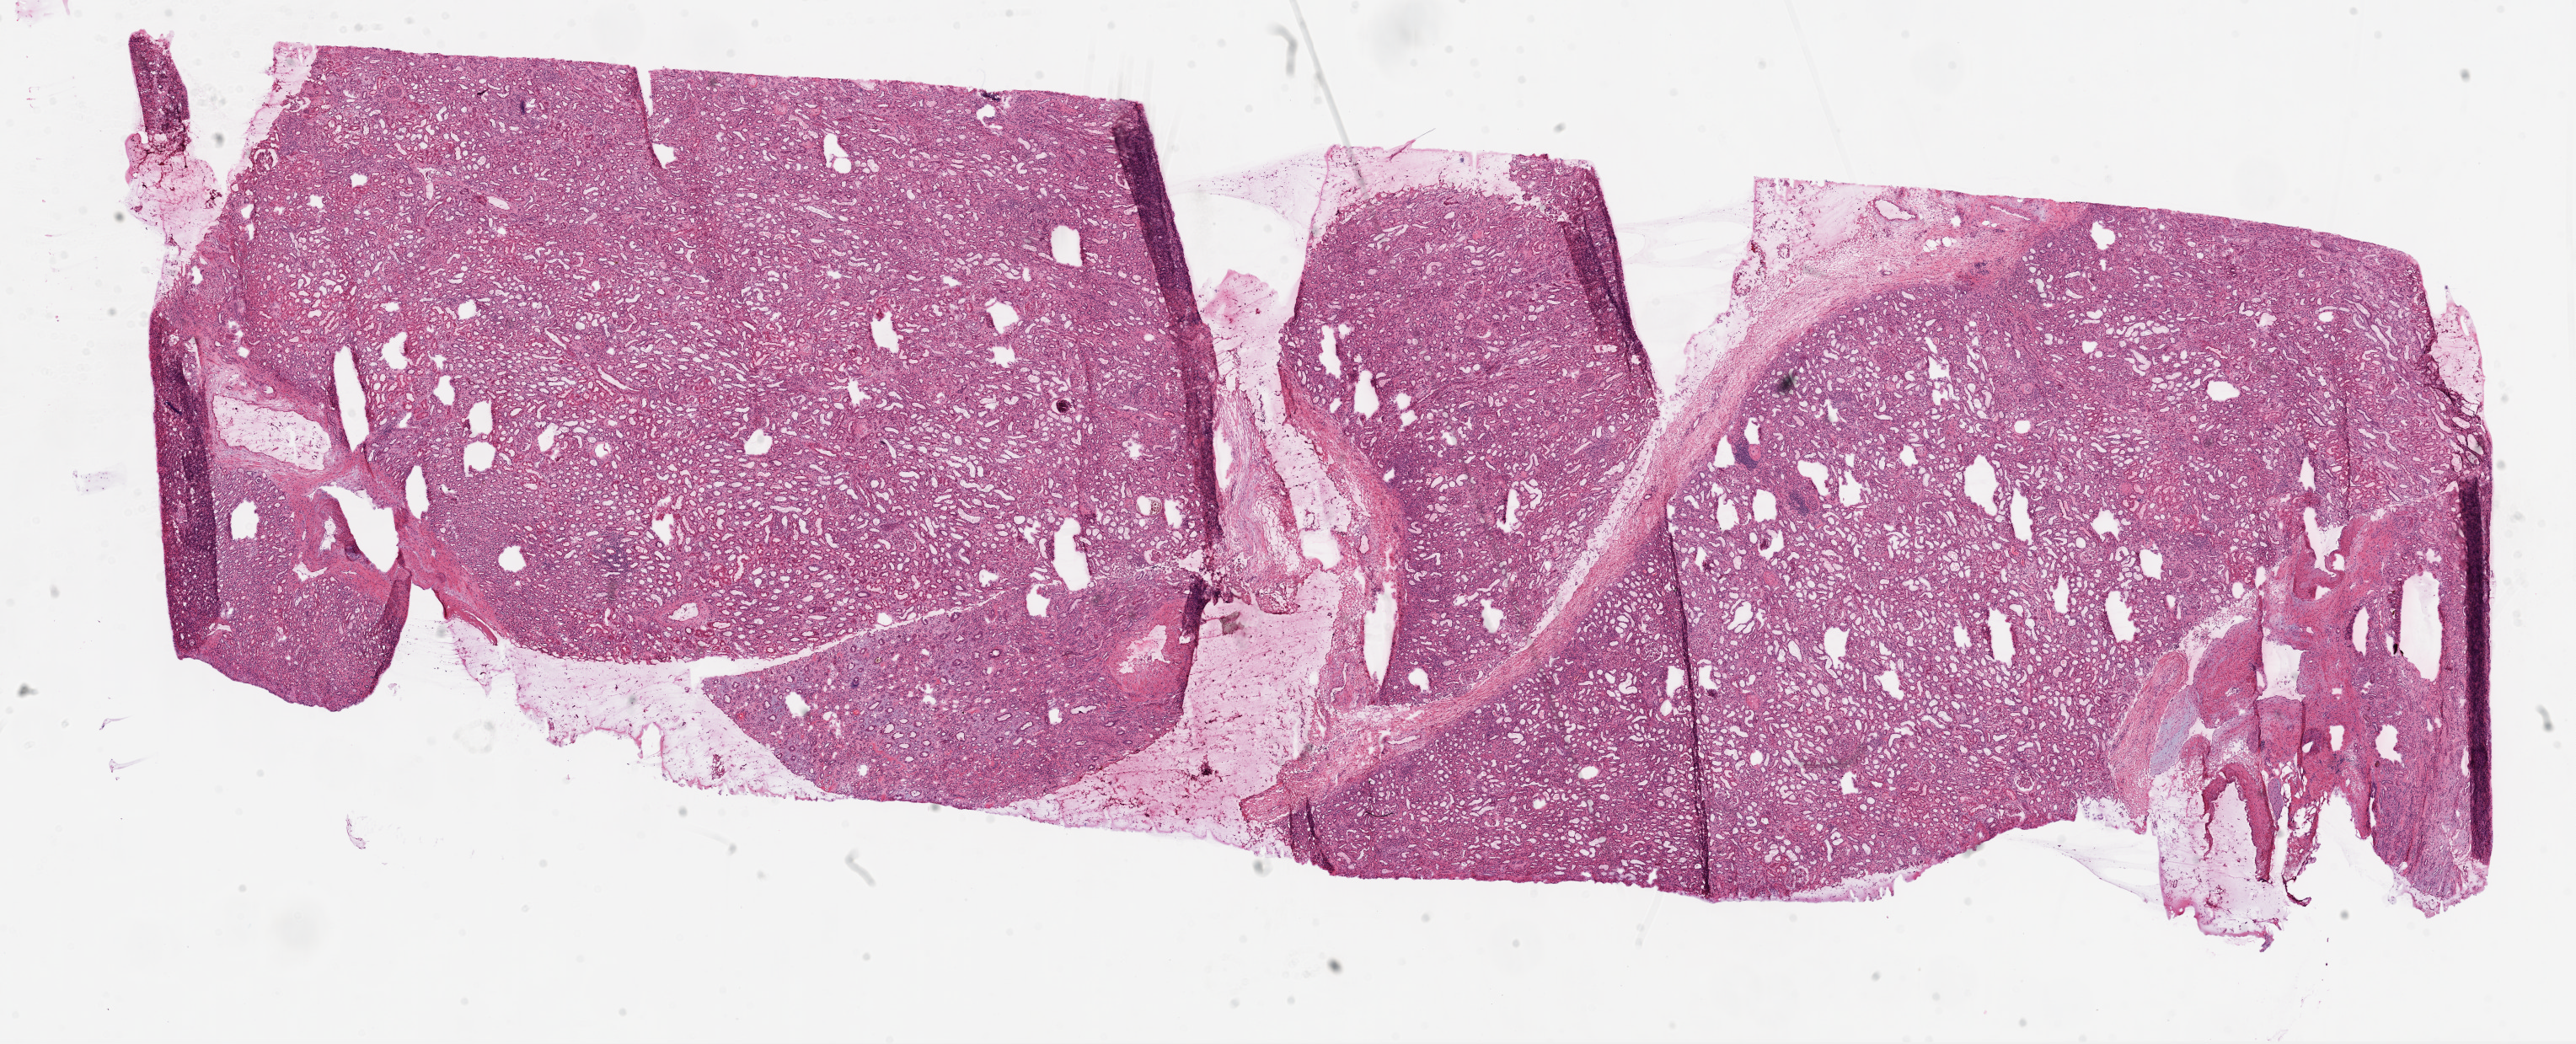
H&E whole-slide image — low-resolution overview of the scanned area, about 24.7 x 10.0 mm (from a 20x scan). Frozen section from the top of the tissue portion. Sample: solid tissue normal (non-tumour tissue), kidney. Female, age 65 years at initial diagnosis.
- this section: solid tissue normal sample (biorepository sample class)
- patient diagnosis: Clear cell adenocarcinoma, NOS